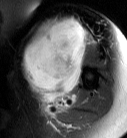
MRI of an extremity soft-tissue mass, one axial slice; slice 50 of 87 in the series (ordered by position); T2-weighted fat-saturated; MR volume resampled by the dataset authors to the PET/CT grid (not the native acquisition matrix); 127 × 138 image matrix, field of view 124 × 135 mm. Female patient. Case-level facts recorded for this patient, not image findings: histological type: pleiomorphic leiomyosarcoma; grade: high; site of the primary tumour: left biceps.
Annotated regions visible in this slice (expert contour drawn on MRI and transferred to this co-registered scan by the dataset authors):
- gross tumour volume including surrounding oedema: box from (x=22, y=16) to (x=91, y=108) px
- gross tumour volume (mass): (x=22, y=18)–(x=87, y=99)